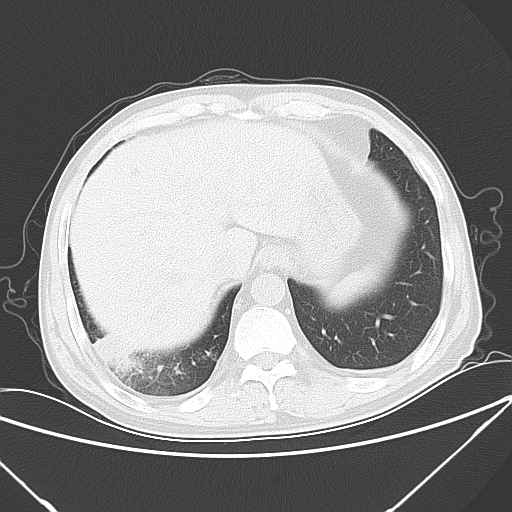
Chest CT, one axial slice; position 14 of 57 along the scan axis; lung window (W 1500 / L -600 HU); 512 × 512 image matrix, field of view 364 × 364 mm. Patient: male, 54 years. Case-level facts recorded for this patient, not image findings: clinical TNM (as recorded): T2 N1 M0; histopathological grade: G3.
Annotated regions visible in this slice (rectangle marked by the reading radiologist):
- lung tumour (recorded histology: adenocarcinoma): box from (x=90, y=329) to (x=139, y=375) px